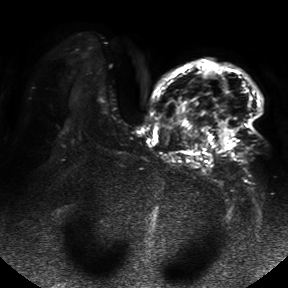
Breast MRI, one axial slice; slice 29 of 50 in the series (ordered by position); diffusion-weighted series; image 2 of 4 stored at this slice position (different b-values; order by instance number); 1.5 T; 4 mm slice thickness; 288 × 288 image matrix, field of view 390 × 390 mm. Female patient.
Outlined on this slice (outlined manually by an expert reader):
- tumour on diffusion-weighted imaging: box from (x=221, y=128) to (x=236, y=151) px